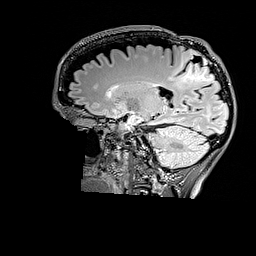
Brain MRI from a brain-tumour surgery series, one sagittal slice. Position 107 of 176 along the scan axis. T2 FLAIR. 1 mm slice thickness. 256 × 256 image matrix, field of view 256 × 256 mm. From the clinical record (not read from this slice): histopathology: Astrocytoma; WHO grade: 3; IDH mutation: yes.
Structures marked on this image (manually delineated by an expert):
- tumour: bounding box <176,49,214,87> (left, top, right, bottom; pixels)
- tumour: <185,59,214,83>